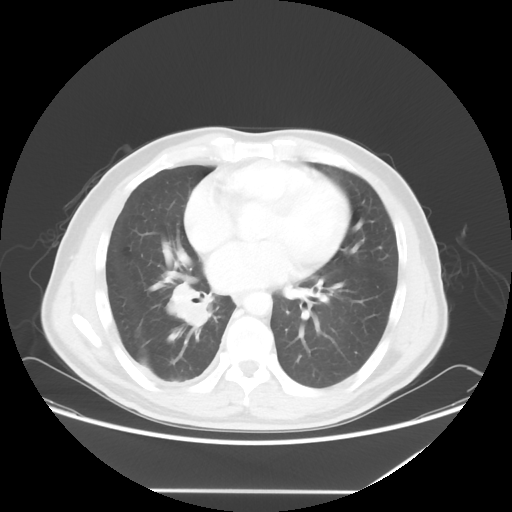
Chest CT, one axial slice; slice 26 of 60 in the series (ordered by position); reconstruction kernel STANDARD; 120 kVp; lung window (W 1500 / L -600 HU); 5 mm slice thickness; 512 × 512 image matrix, field of view 419 × 419 mm. Patient: male, 48 years. From the clinical record (not read from this slice): clinical TNM (as recorded): T3 N3 M1a.
Outlined on this slice (bounding box drawn by a radiologist):
- lung tumour (recorded histology: squamous cell carcinoma): bounding box (x1, y1, x2, y2) in pixels: (158, 282, 217, 336)